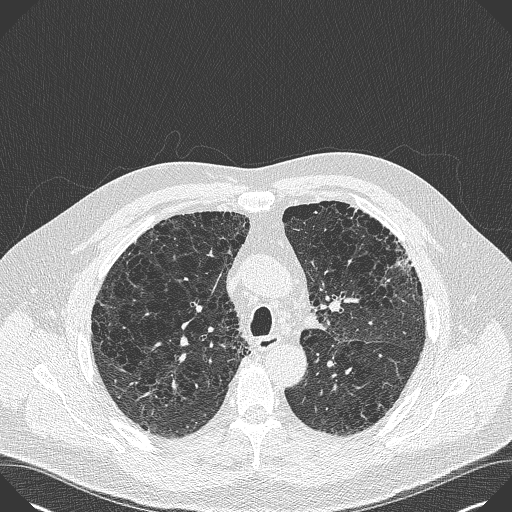
Chest CT (low-dose screening protocol), one axial image, baseline annual screen, lung window (W 1500 / L -600 HU), lung (sharp) reconstruction kernel (B50f), 512 × 512 image matrix. Male participant, aged 59 years at enrolment. Current smoker at enrolment.
• Lesion marked by an expert reader, box from (x=376, y=236) to (x=427, y=287) px.
• Screening reader's record for this exam: no non-calcified nodule ≥4 mm recorded.
• Lung cancer was diagnosed 909 days after this screen: bronchiolo-alveolar carcinoma, mixed mucinous and non-mucinous, left upper lobe, stage IA (AJCC 6th edition), 20 mm at pathology.